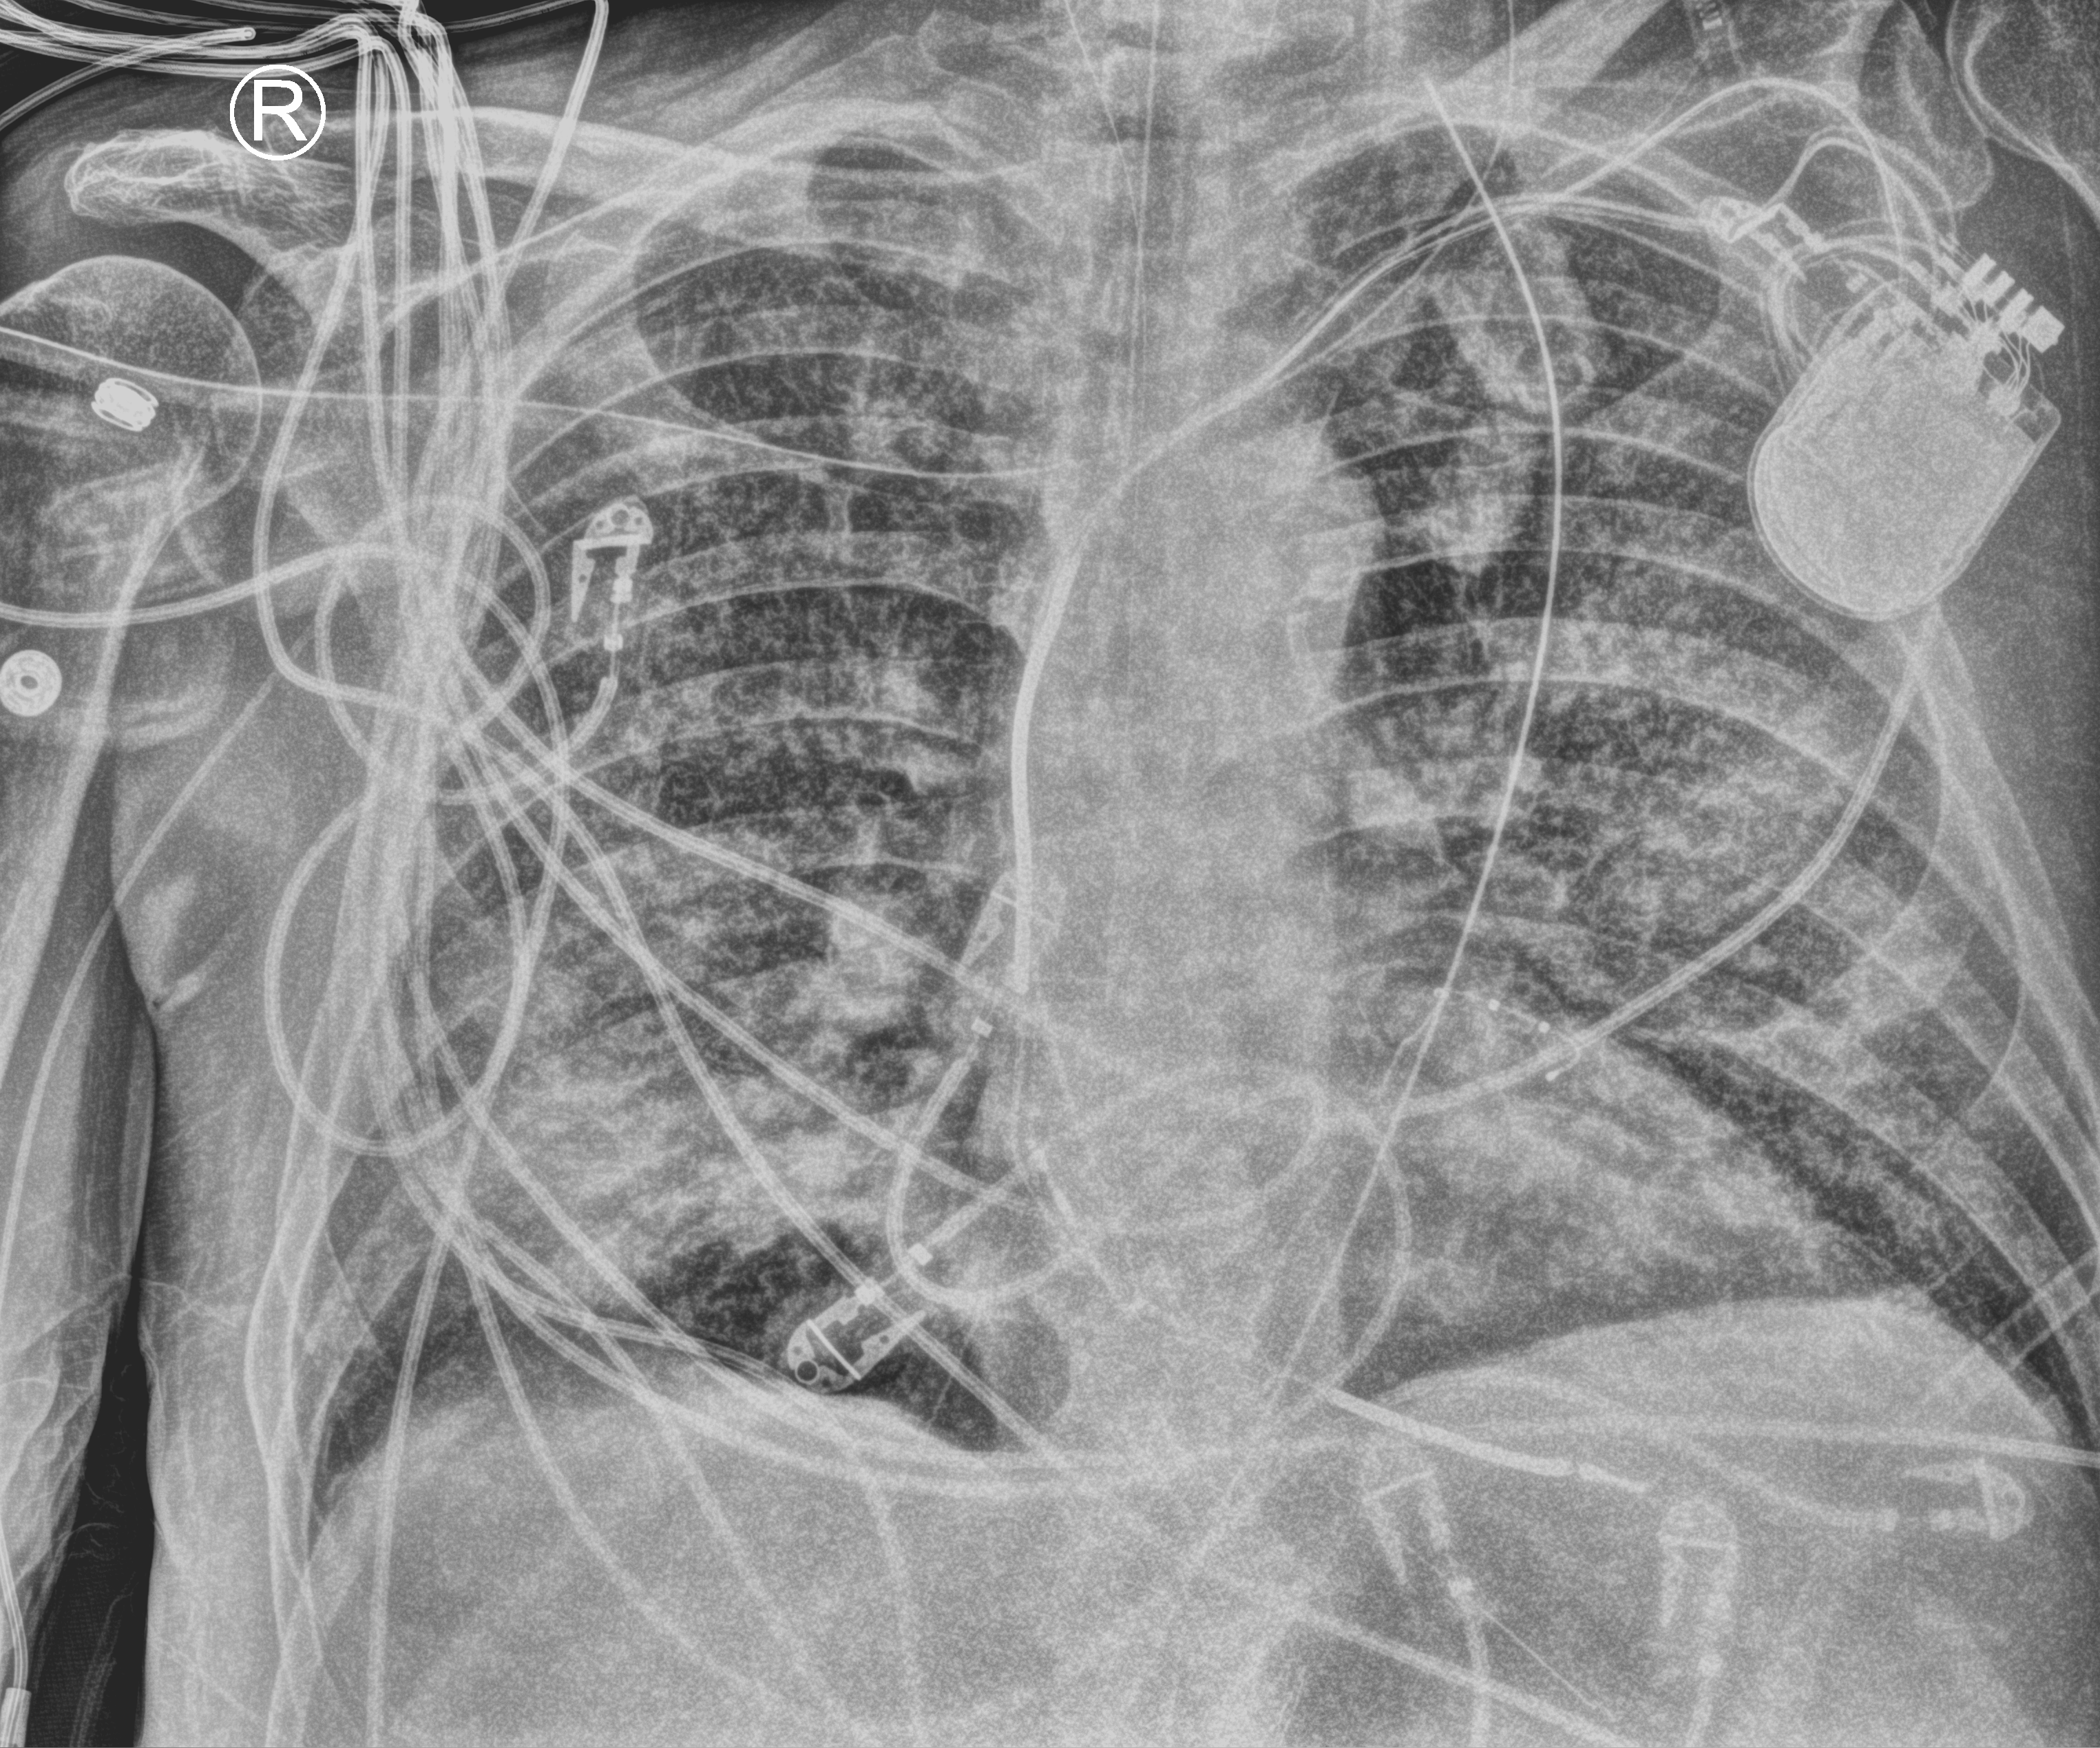
Portable chest radiograph, anteroposterior (AP) projection. Male patient hospitalised with COVID-19, age 60–74 years.
Admission-level facts for this patient (not findings on this image; timing relative to this image not recorded):
- chronic kidney disease (admission record): no